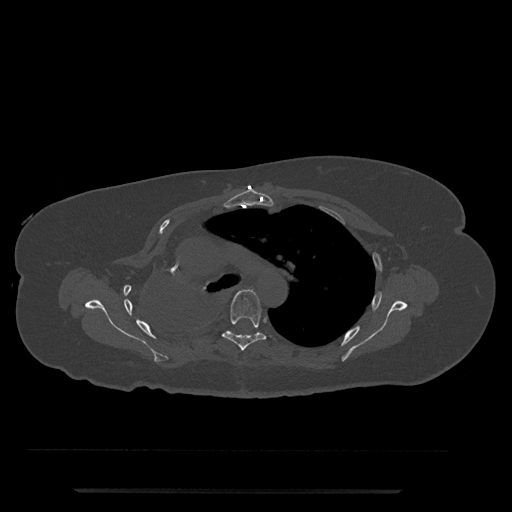
CT including the spine, one axial slice. Slice 544 of 797 in the series (ordered by position). Reconstruction kernel Br40s/3. 120 kVp. Bone window (W 1800 / L 400 HU). 512 × 512 image matrix, field of view 440 × 440 mm. Patient: female, 51 years. From the clinical record (not read from this slice): primary cancer: neuro; vertebrae with lytic lesions (as recorded): T8.
Structures marked on this image (semi-automatic segmentation, software-assisted and operator-edited):
- T5 vertebra: box from (x=222, y=289) to (x=266, y=351) px